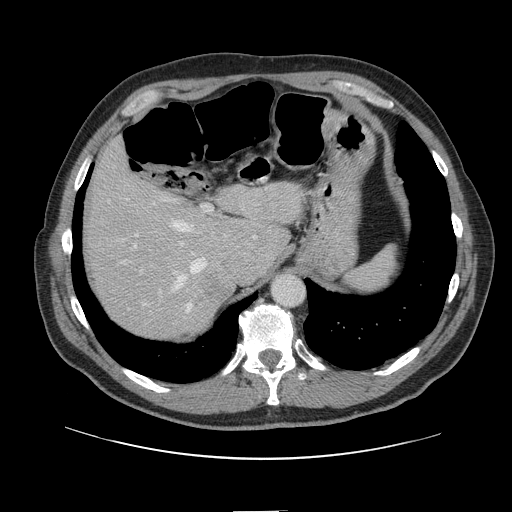
Contrast-enhanced abdominal CT, one axial slice. Slice 106 of 161 in the series (ordered by position). Soft-tissue window (W 400 / L 40 HU). 512 × 512 image matrix, field of view 412 × 412 mm. Male patient, age 66 years. Case-level facts recorded for this patient, not image findings: diagnosis: colorectal cancer liver metastases, imaged before liver resection; multiple liver metastases: no; largest metastasis: 3.5 cm.
Annotated regions visible in this slice (expert manual segmentation):
- hepatic veins: bounding box <109,200,208,313> (left, top, right, bottom; pixels)
- liver: <88,145,303,338>
- planned liver remnant (the part of the liver to remain after resection): <88,145,303,307>
- portal vein (with intrahepatic branches): <132,204,213,296>
- liver metastasis: <196,270,227,312>